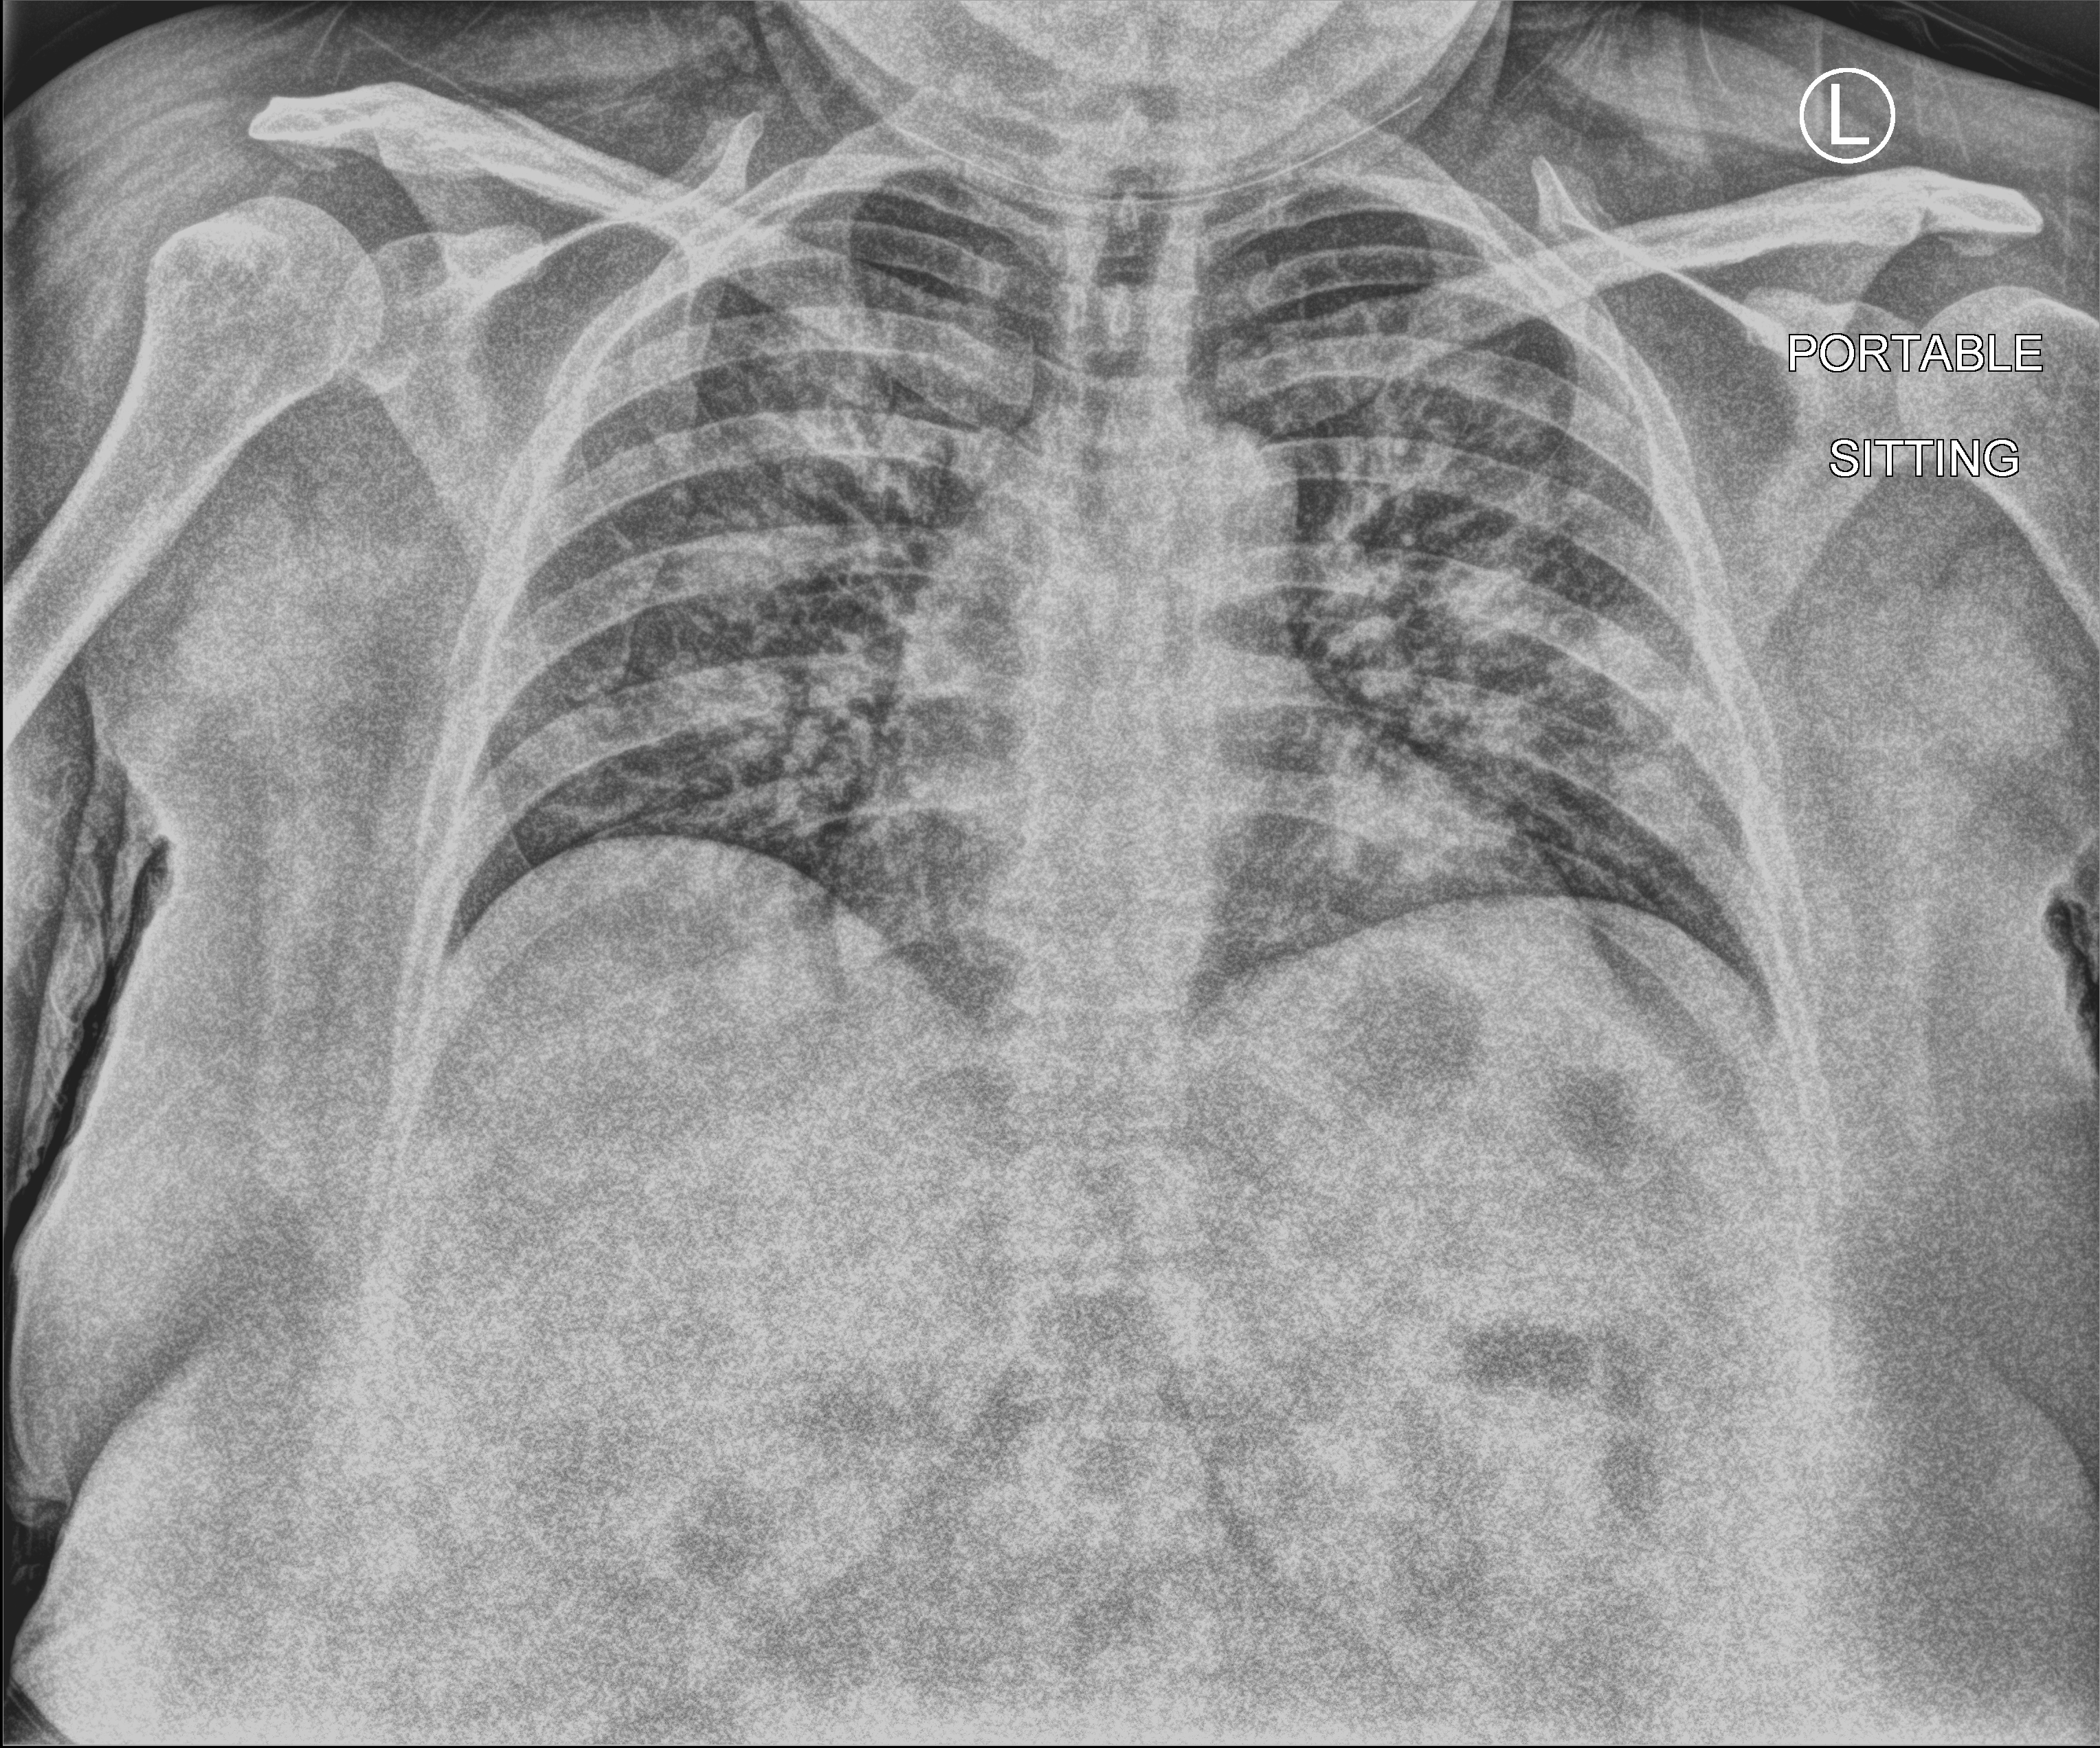
Bedside chest radiograph (computed radiography). Patient hospitalised with COVID-19; female, aged 18–59 years.
Admission-level facts for this patient (not findings on this image; timing relative to this image not recorded): mechanically ventilated during this hospital stay: no; hypertension (admission record): yes; admitted to intensive care during this hospital stay: no.